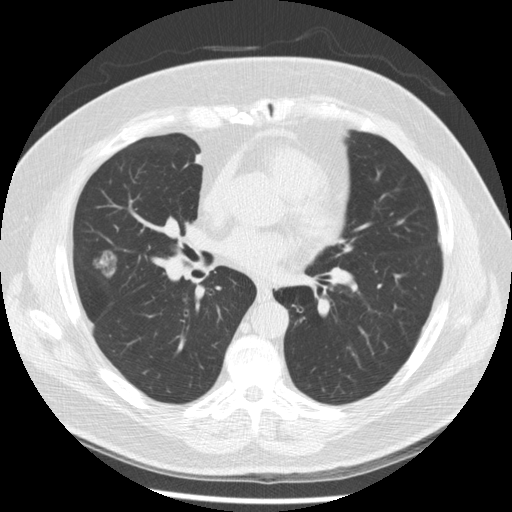
Low-dose screening chest CT, axial slice; second annual screen; lung window (W 1500 / L -600 HU); 2.5 mm slice thickness; 120 kVp. Male, age 67 years at enrolment.
Expert reader's lesion annotation, bounding box (x1, y1, x2, y2) in pixels: (81, 245, 123, 287). The exam's reader record, not a measurement of the box and not confirmed to be the same lesion: non-calcified nodule or mass ≥4 mm, right middle lobe, 19 × 16 mm, smooth margins, soft tissue attenuation, pre-existing on the prior screen: yes; interval growth: yes. Later outcome: lung cancer diagnosed 47 days after this screen — adenocarcinoma, NOS, right middle lobe, moderately differentiated (G2), stage IA (AJCC 6th edition), 14 mm at pathology.